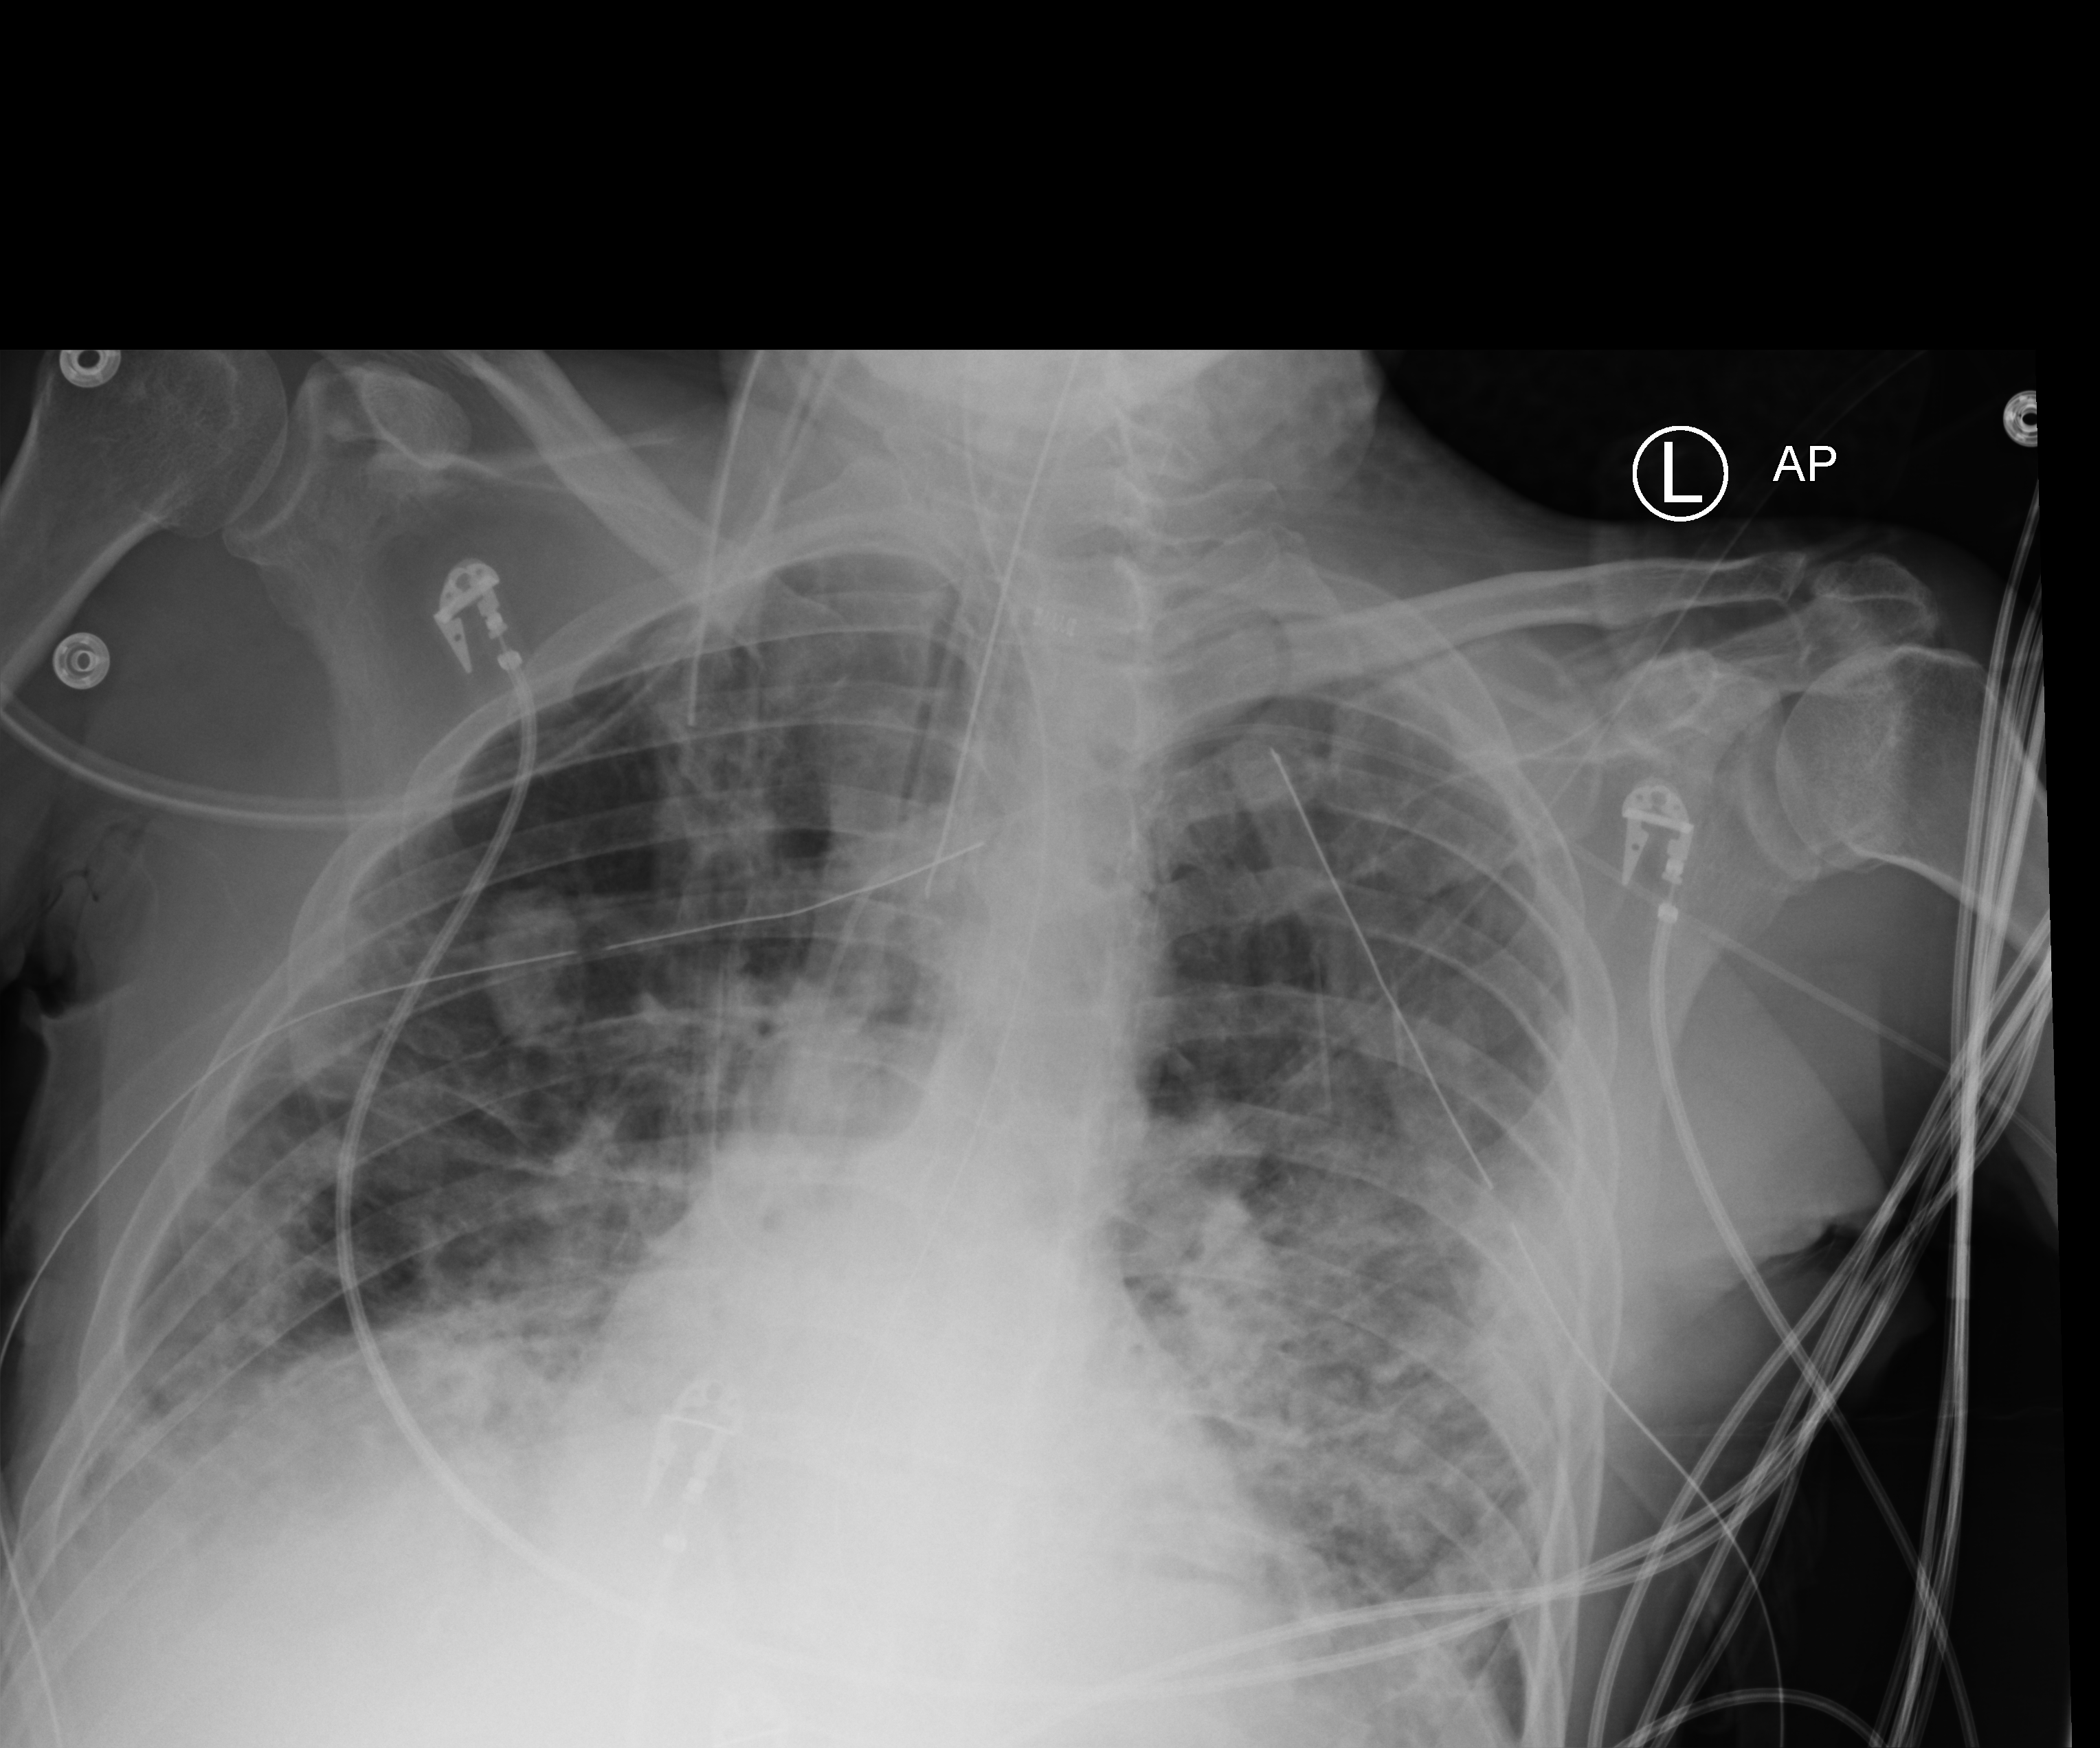
Bedside chest radiograph (computed radiography); anteroposterior (AP) projection. Patient hospitalised with COVID-19; male, aged 18–59 years.
From the hospital-stay record, not from the radiograph (when in the stay this image was taken is not recorded):
- diabetes (admission record): yes